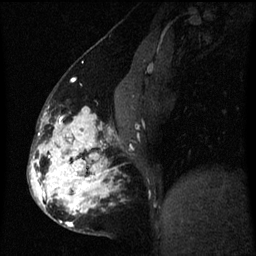
Breast MRI (dynamic contrast-enhanced), one sagittal slice. Slice 26 of 60 in the series (ordered by position). Dynamic contrast-enhanced series, image 2 of 3 at this slice position (ordered by acquisition). 1.5 T. TE 4.2 ms, TR 8 ms. 256 × 256 image matrix, field of view 190 × 190 mm. Patient: female, 50 years.
Structures marked on this image (semi-automatic segmentation, software-assisted and operator-edited):
- analysis volume of interest (the breast-tissue region the enhancement analysis was run in; not a lesion): bounding box <32,107,117,233> (left, top, right, bottom; pixels)
- tumour enhancement mask (voxels above the 70 % enhancement threshold inside the analysis volume of interest): <32,107,109,227>